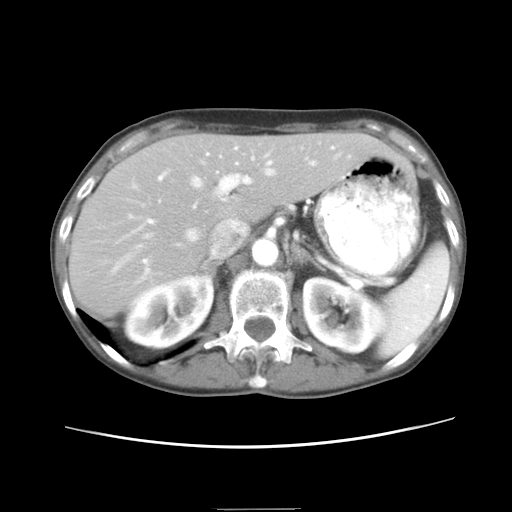
Contrast-enhanced abdominal CT, one axial slice; slice 15 of 26 in the series (ordered by position); reconstruction kernel STANDARD; 120 kVp; intravenous contrast given; soft-tissue window (W 400 / L 40 HU); 7.5 mm slice thickness; 512 × 512 image matrix, field of view 340 × 340 mm. Female patient, age 65 years. From the clinical record (not read from this slice): diagnosis: colorectal cancer liver metastases, imaged before liver resection; multiple liver metastases: no.
Structures marked on this image (expert manual segmentation):
- hepatic veins: bounding box (x1, y1, x2, y2) in pixels: (114, 154, 315, 301)
- liver: (71, 133, 384, 313)
- planned liver remnant (the part of the liver to remain after resection): (71, 133, 383, 313)
- portal vein (with intrahepatic branches): (148, 146, 271, 223)